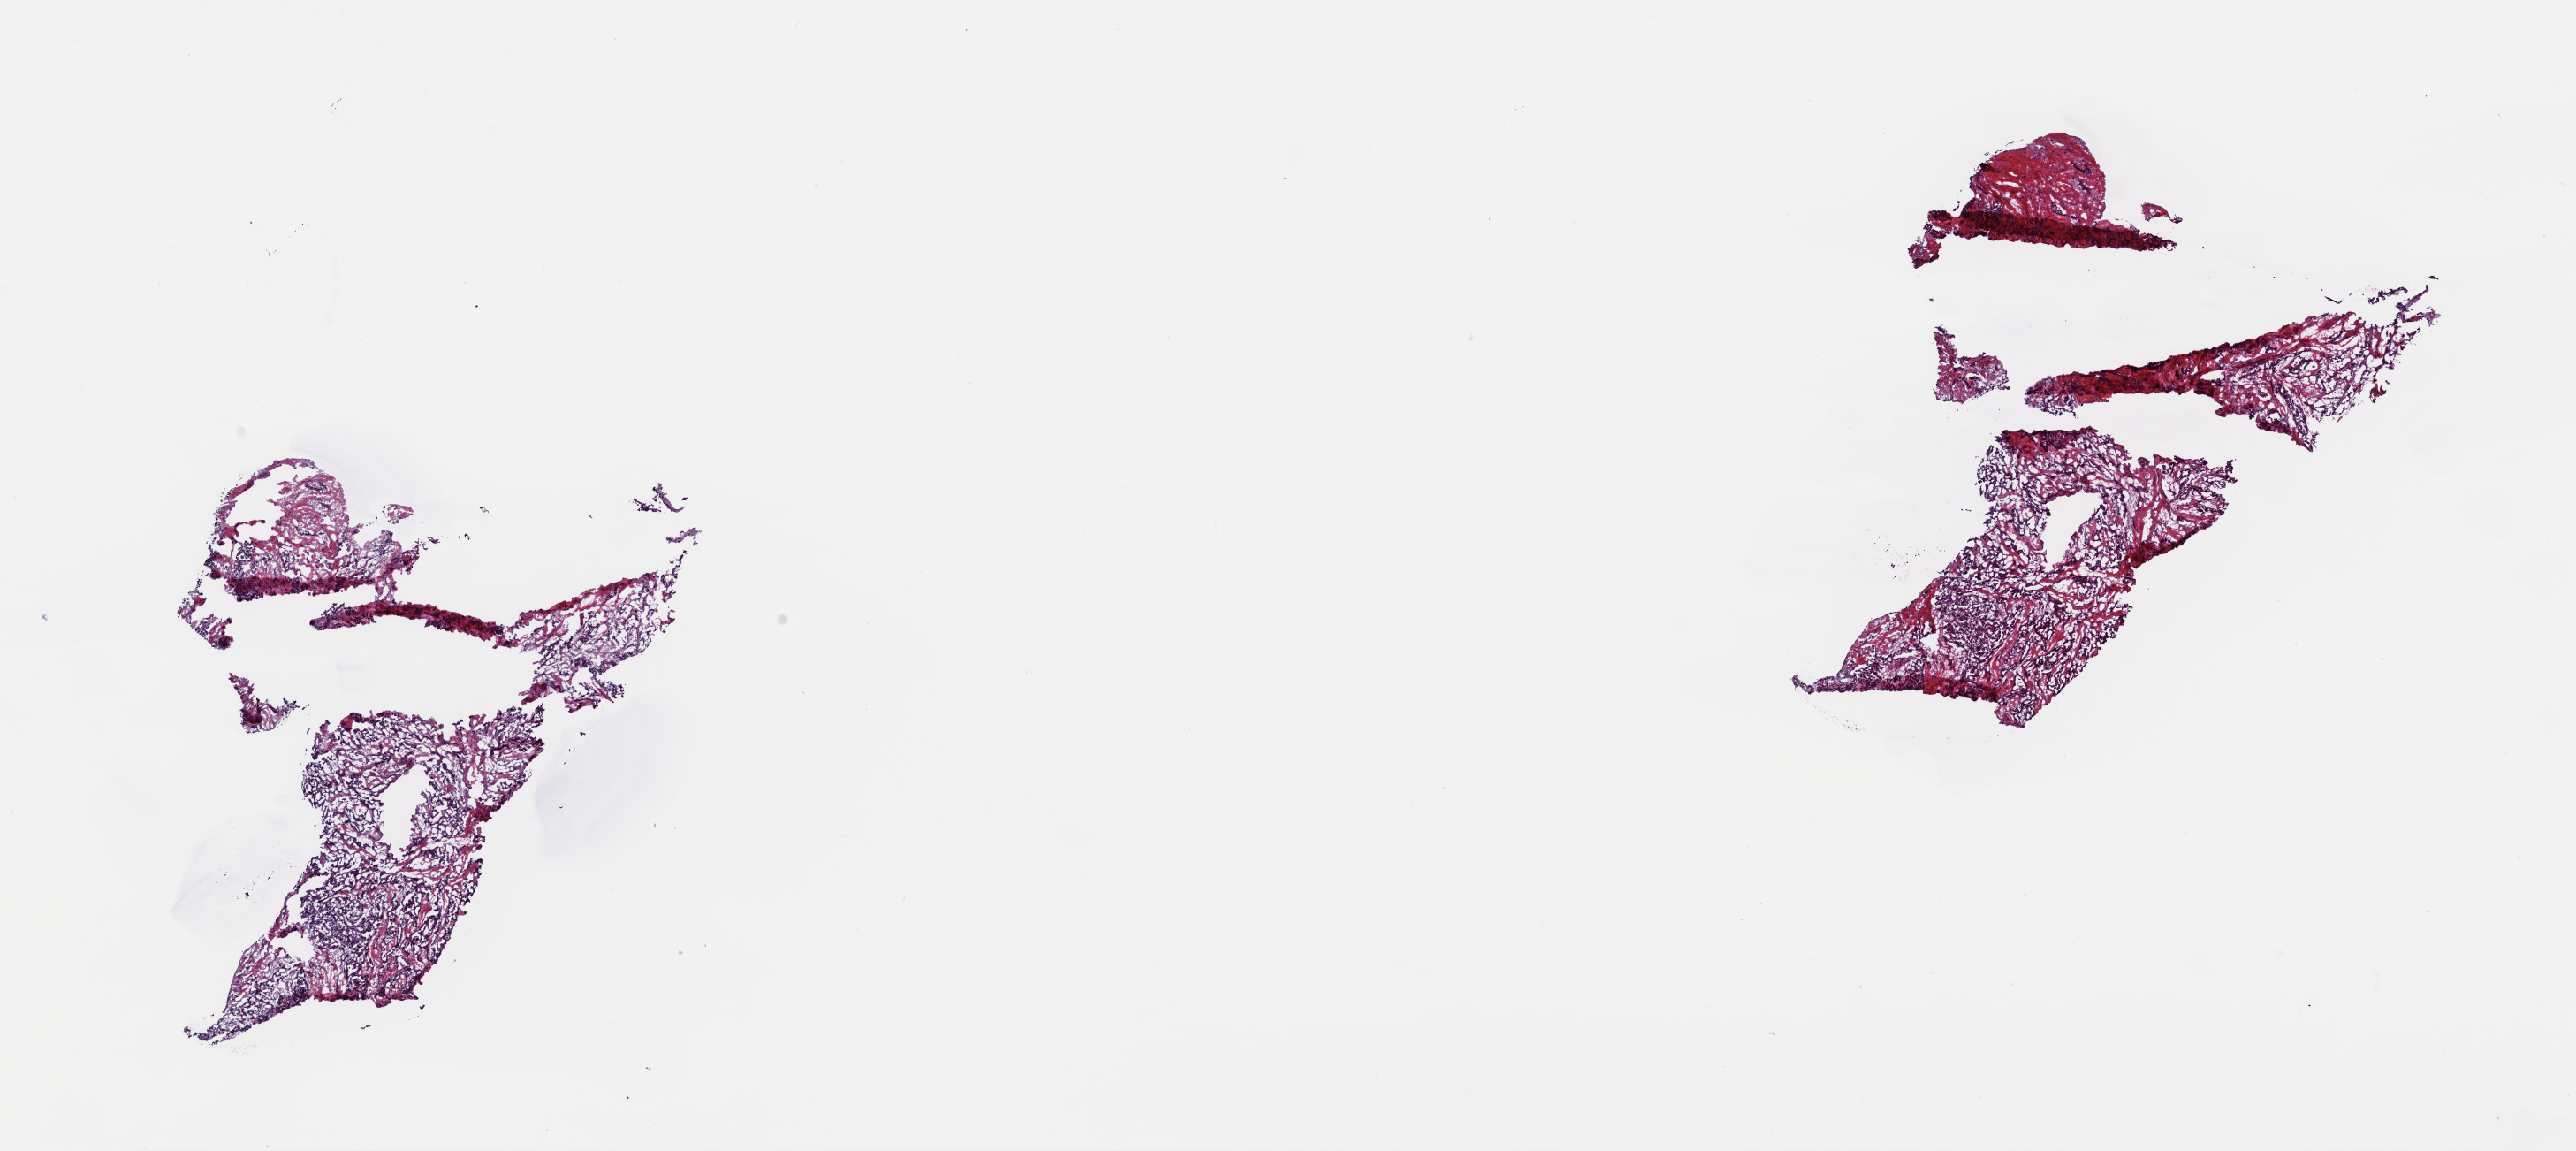
Whole-slide histology image, H&E-stained, shown as a low-resolution overview of the whole scanned area (about 23.0 x 10.3 mm, slide scanned at 40x). Frozen section from the top of the tissue portion. Primary tumour sample from the thyroid. Female patient; age at initial diagnosis 57 years. Slide review estimates, as recorded: tumour cells 85%, tumour nuclei 85%, normal cells 0%, stromal cells 15%, necrosis 0%. Inflammatory infiltration, as recorded: lymphocyte infiltration 3%, monocyte infiltration 0%, neutrophil infiltration 0%.
• lymph nodes positive (case pathology): 6 of 48 examined
• pathologic diagnosis: Papillary adenocarcinoma, NOS
• laterality: right
• AJCC pathologic stage: IVA (6th edition)